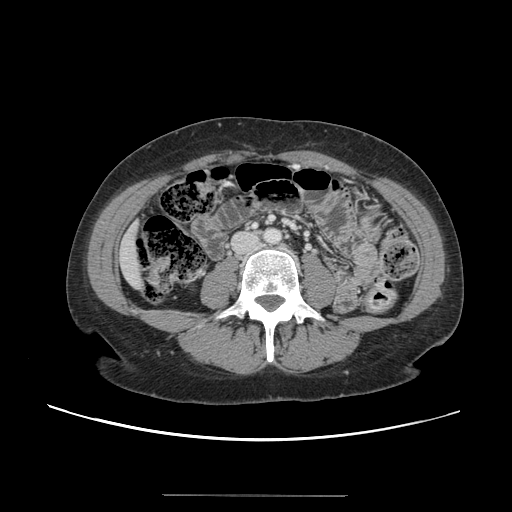
Contrast-enhanced abdominal CT, one axial slice; slice 18 of 144 in the series (ordered by position); soft-tissue window (W 400 / L 40 HU); 2.5 mm slice thickness; 512 × 512 image matrix, field of view 380 × 380 mm. Female patient, age 53 years. From the clinical record (not read from this slice): diagnosis: colorectal cancer liver metastases, imaged before liver resection; multiple liver metastases: yes; largest metastasis: 1.1 cm; disease in both lobes: no.
Structures marked on this image (manually delineated by an expert):
- liver: bounding box <119,224,143,289> (left, top, right, bottom; pixels)
- planned liver remnant (the part of the liver to remain after resection): <119,225,143,290>